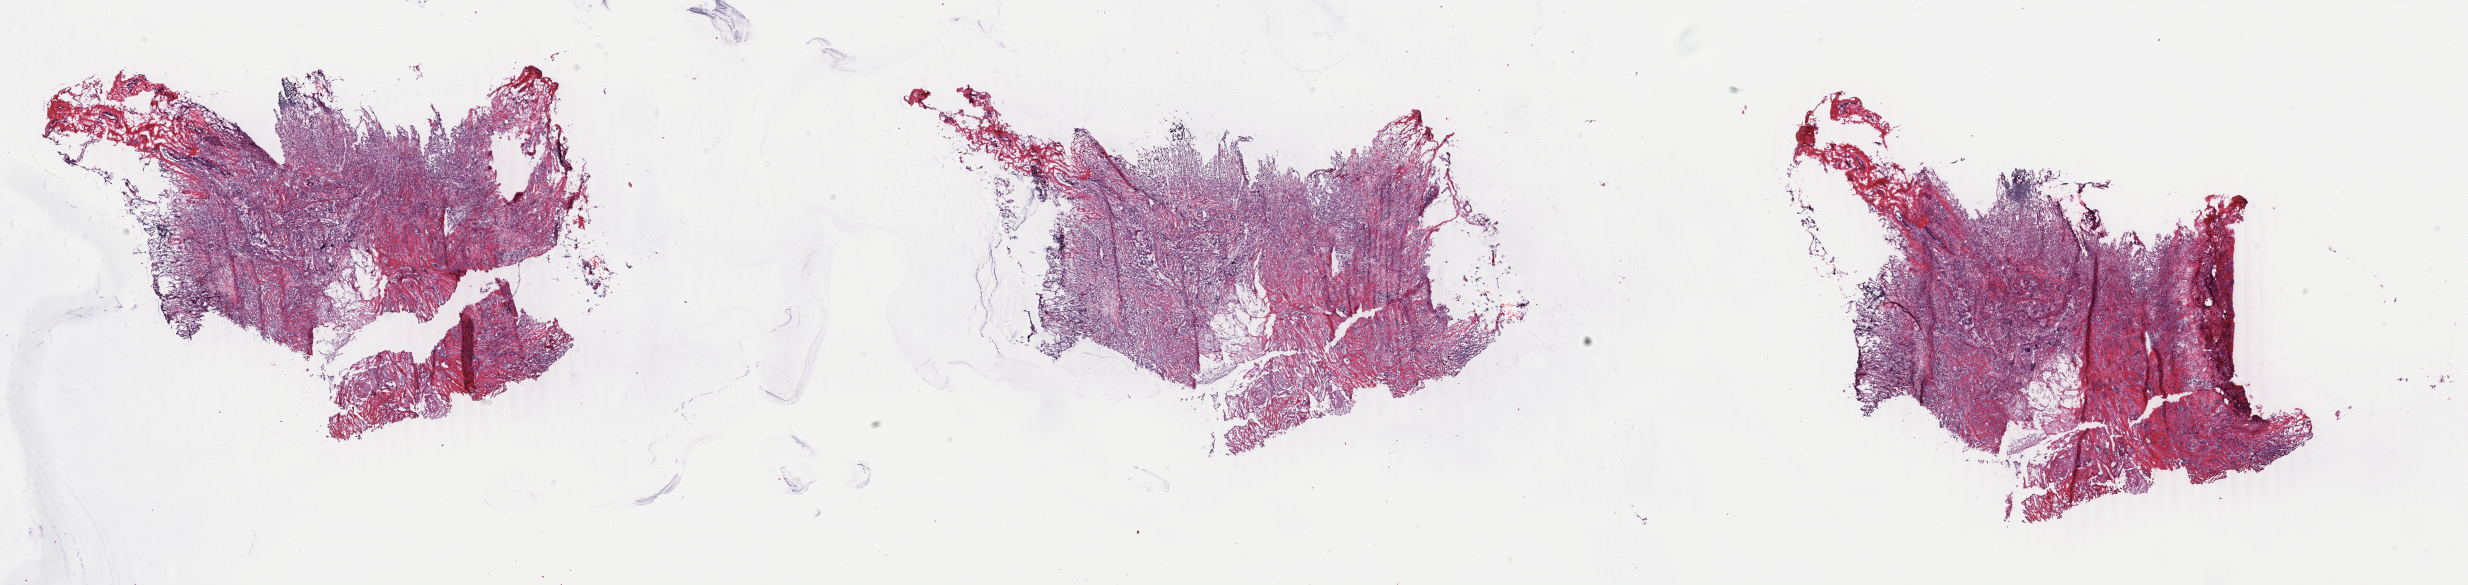
Whole-slide histology image, Hematoxylin and eosin (H&E) stained, low-resolution overview of the scanned area, about 39.3 x 9.3 mm; frozen section; sample: primary tumour, breast. Female patient; age at initial diagnosis 61 years. Pathologist review of this section (percent, as recorded): tumour cells 73%, tumour nuclei 80%, normal cells 0%, stromal cells 27%, necrosis 0%. Infiltration values recorded for this section: lymphocyte infiltration 2%, monocyte infiltration 0%, neutrophil infiltration 0%.
AJCC pathologic stage: IA (7th edition). Pathologic diagnosis: Infiltrating duct carcinoma, NOS. Laterality: right.